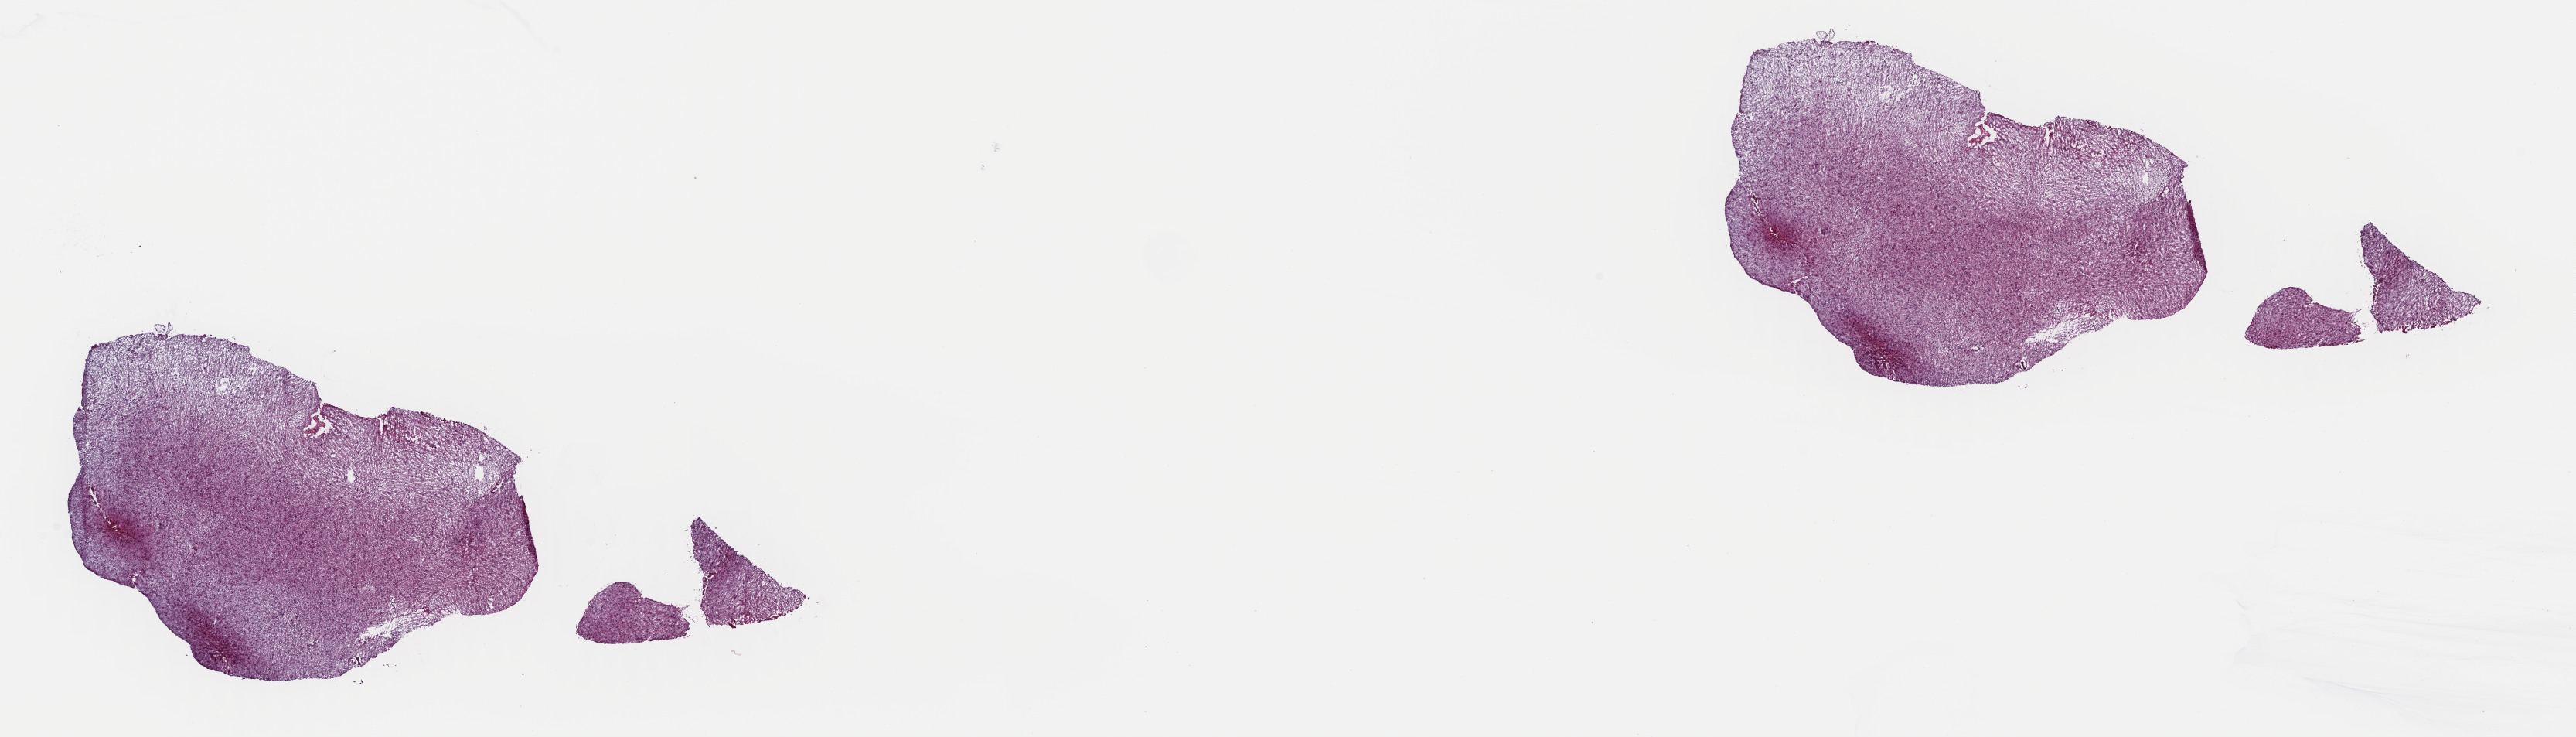
Digitized H&E-stained tissue section (whole slide), whole scanned area (about 26.3 x 7.5 mm, acquisition: 40x scan) shown as a low-resolution overview; frozen section; sample: primary tumour, brain. Female patient; age at initial diagnosis 70 years. Histologic grade: G3 (poorly differentiated). Slide review estimates, as recorded: tumour cells 70%, tumour nuclei 85%, normal cells 5%, stromal cells 25%, necrosis 0%. Inflammatory infiltration, as recorded: lymphocyte infiltration 0%, monocyte infiltration 0%, neutrophil infiltration 0%.
Diagnosis: Astrocytoma, anaplastic. Laterality: left.